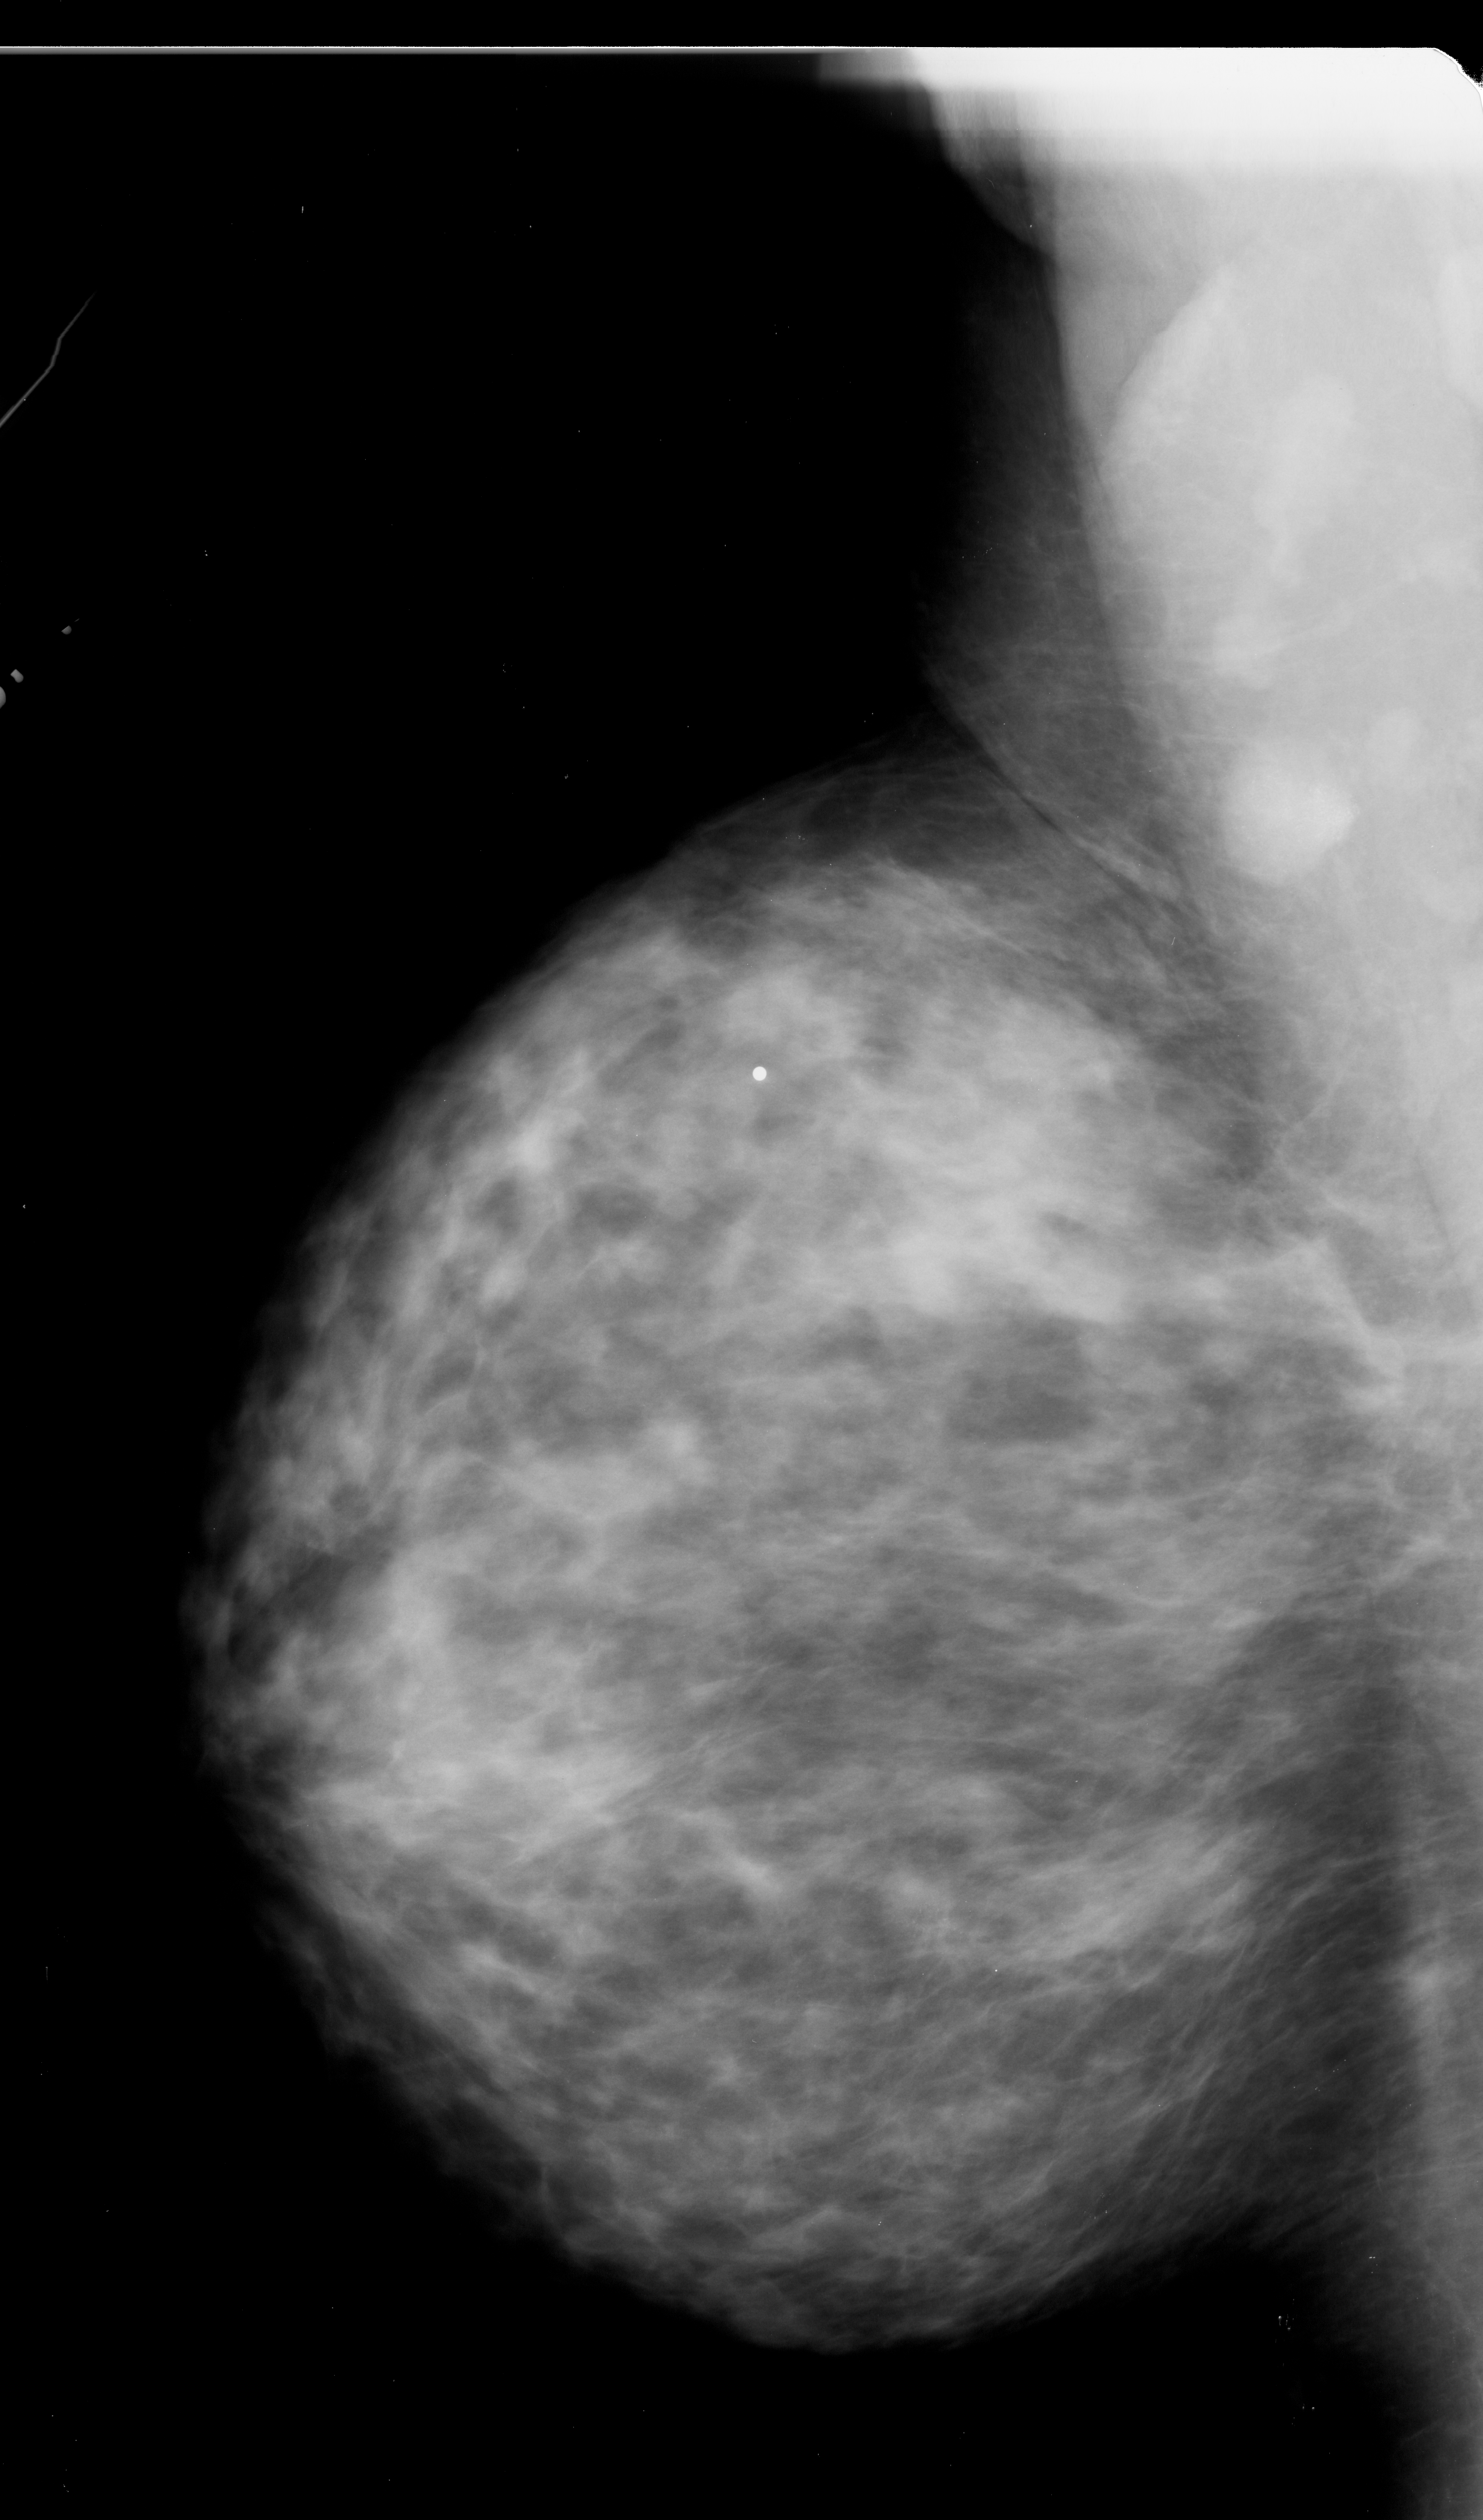
Digitized screen-film mammogram. Left breast. Mediolateral oblique (MLO) view. 1483 × 2520 image matrix.
Marked abnormalities (boxes around the expert regions of interest):
- calcifications, morphology pleomorphic, distribution clustered; BI-RADS assessment category 4; subtlety rating 1 on a 1 (subtle) to 5 (obvious) scale; pathology (as recorded): malignant: box from (x=886, y=1880) to (x=988, y=1952) px